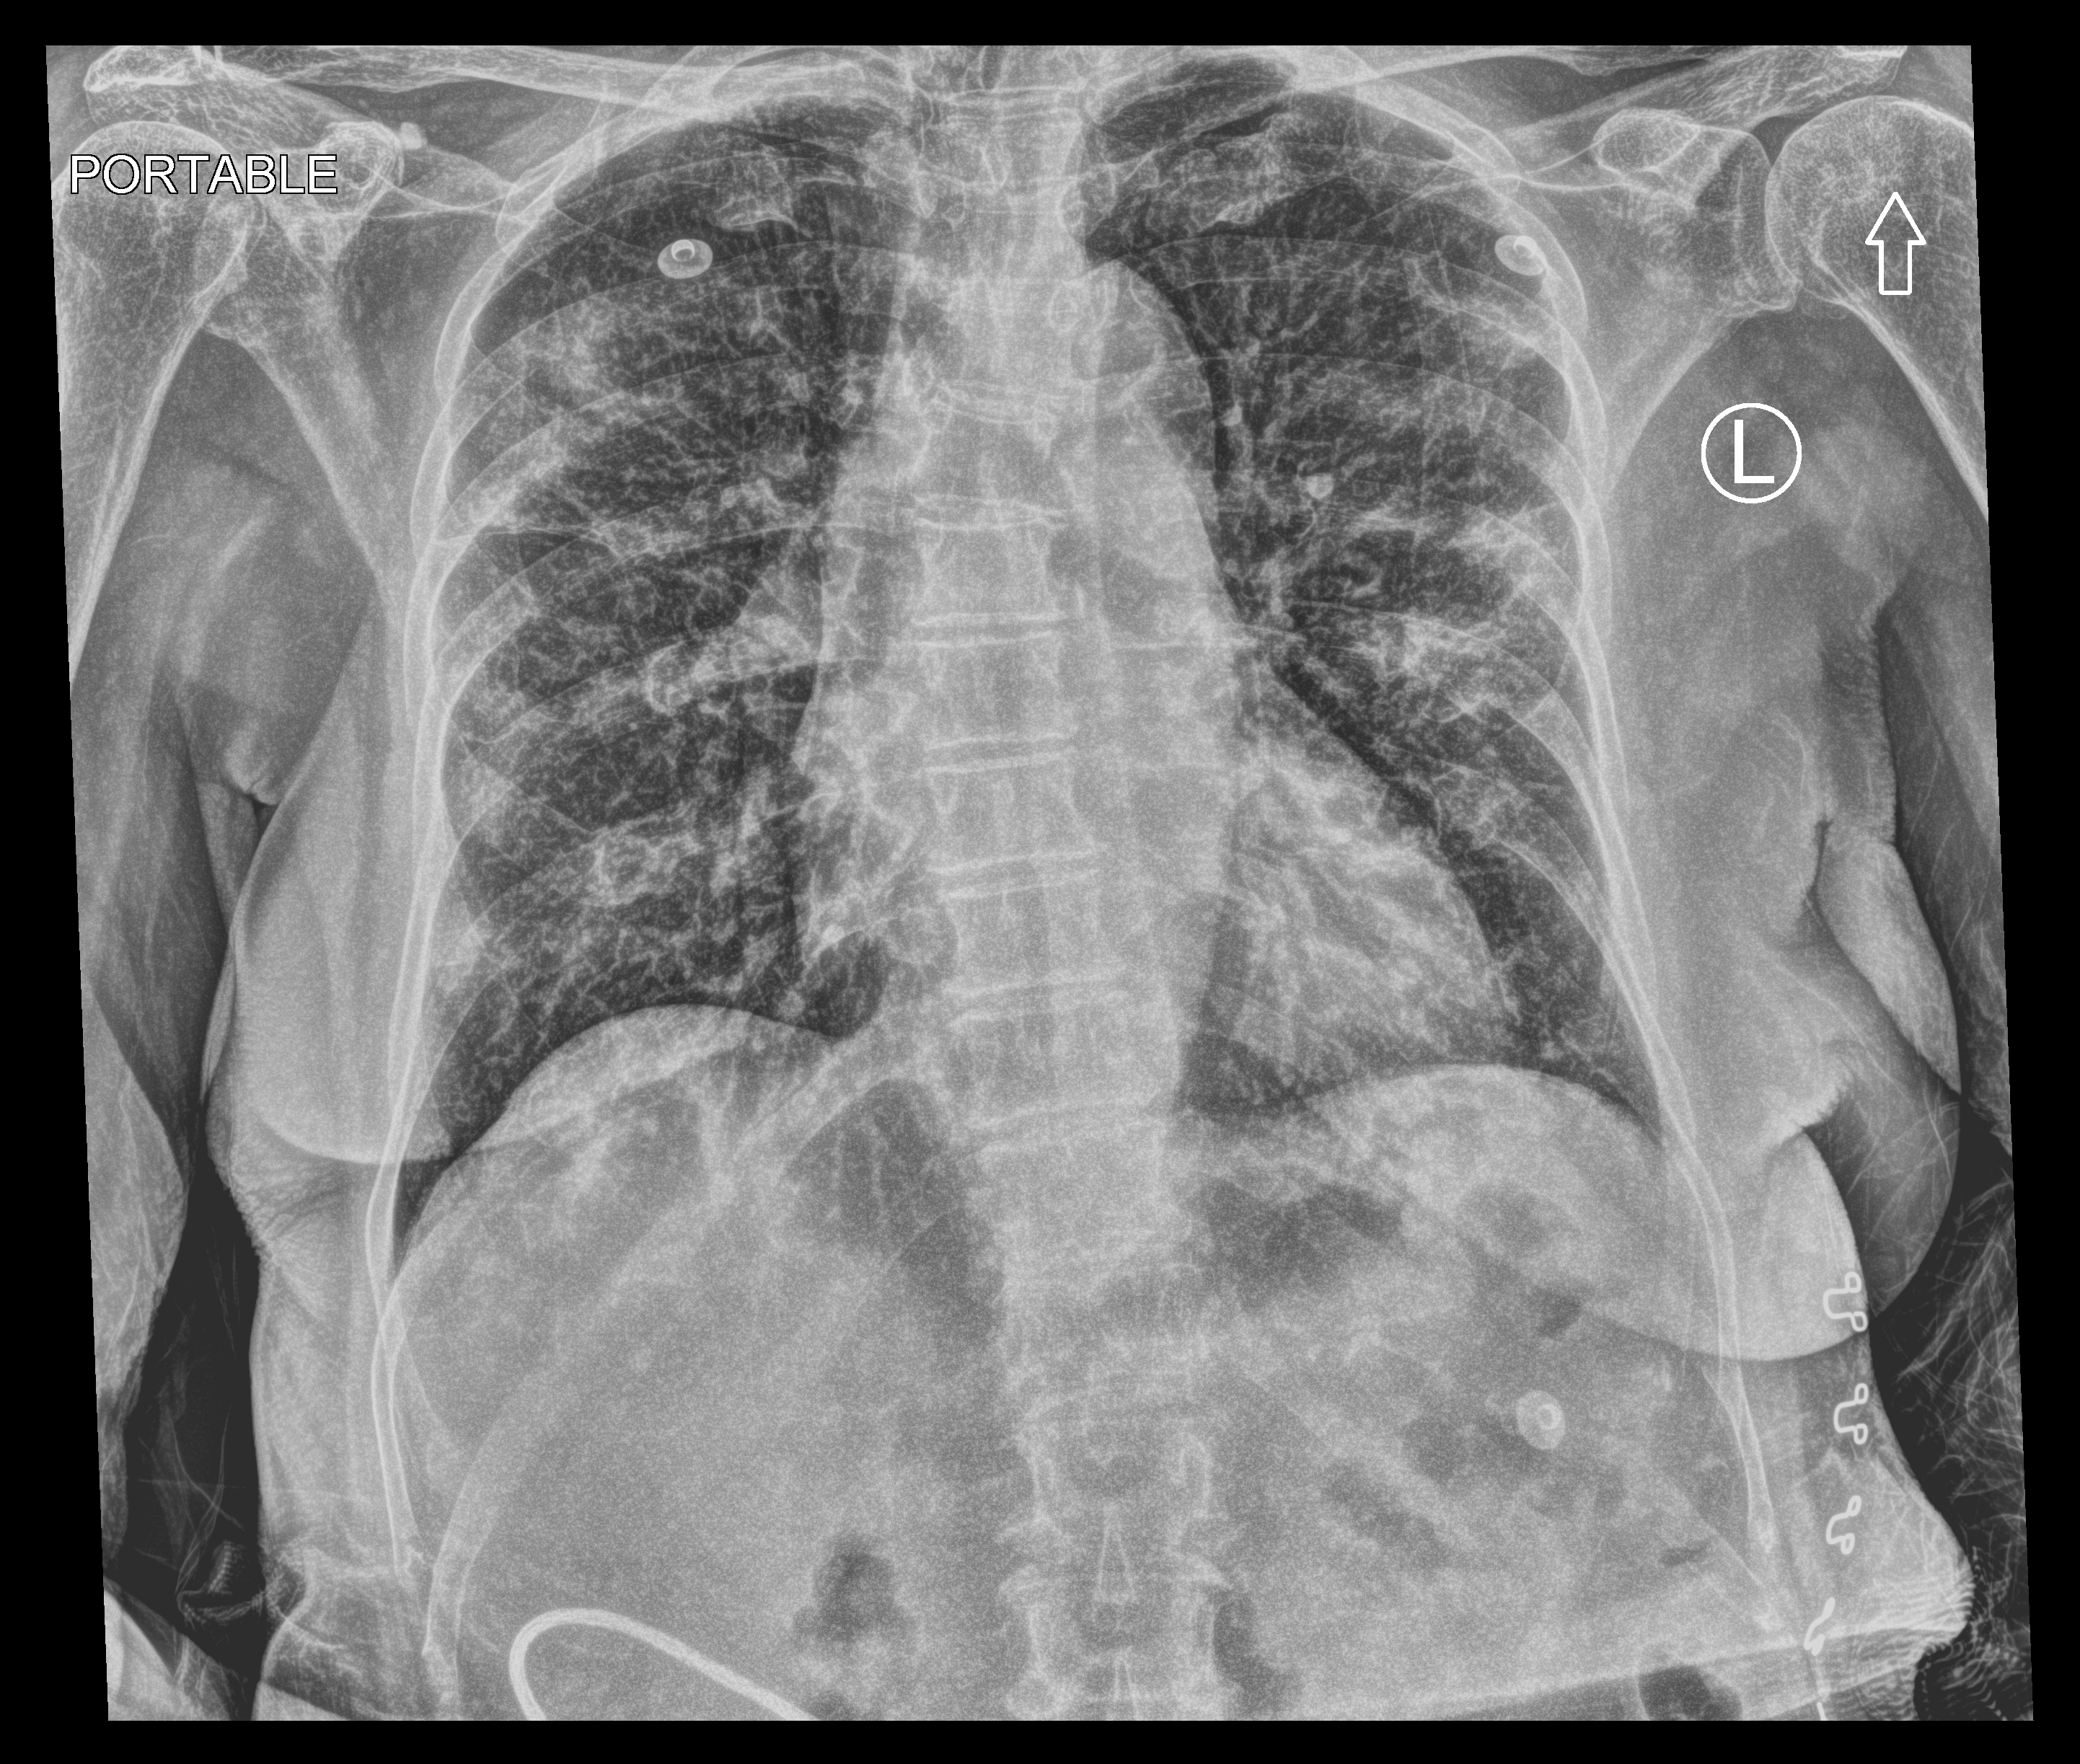
Bedside chest radiograph (computed radiography); anteroposterior (AP) projection. Female patient hospitalised with COVID-19, age 75–90 years.
Hospital-stay facts (about this admission, not read from this image; timing relative to this image not recorded):
- mechanically ventilated during this hospital stay: no